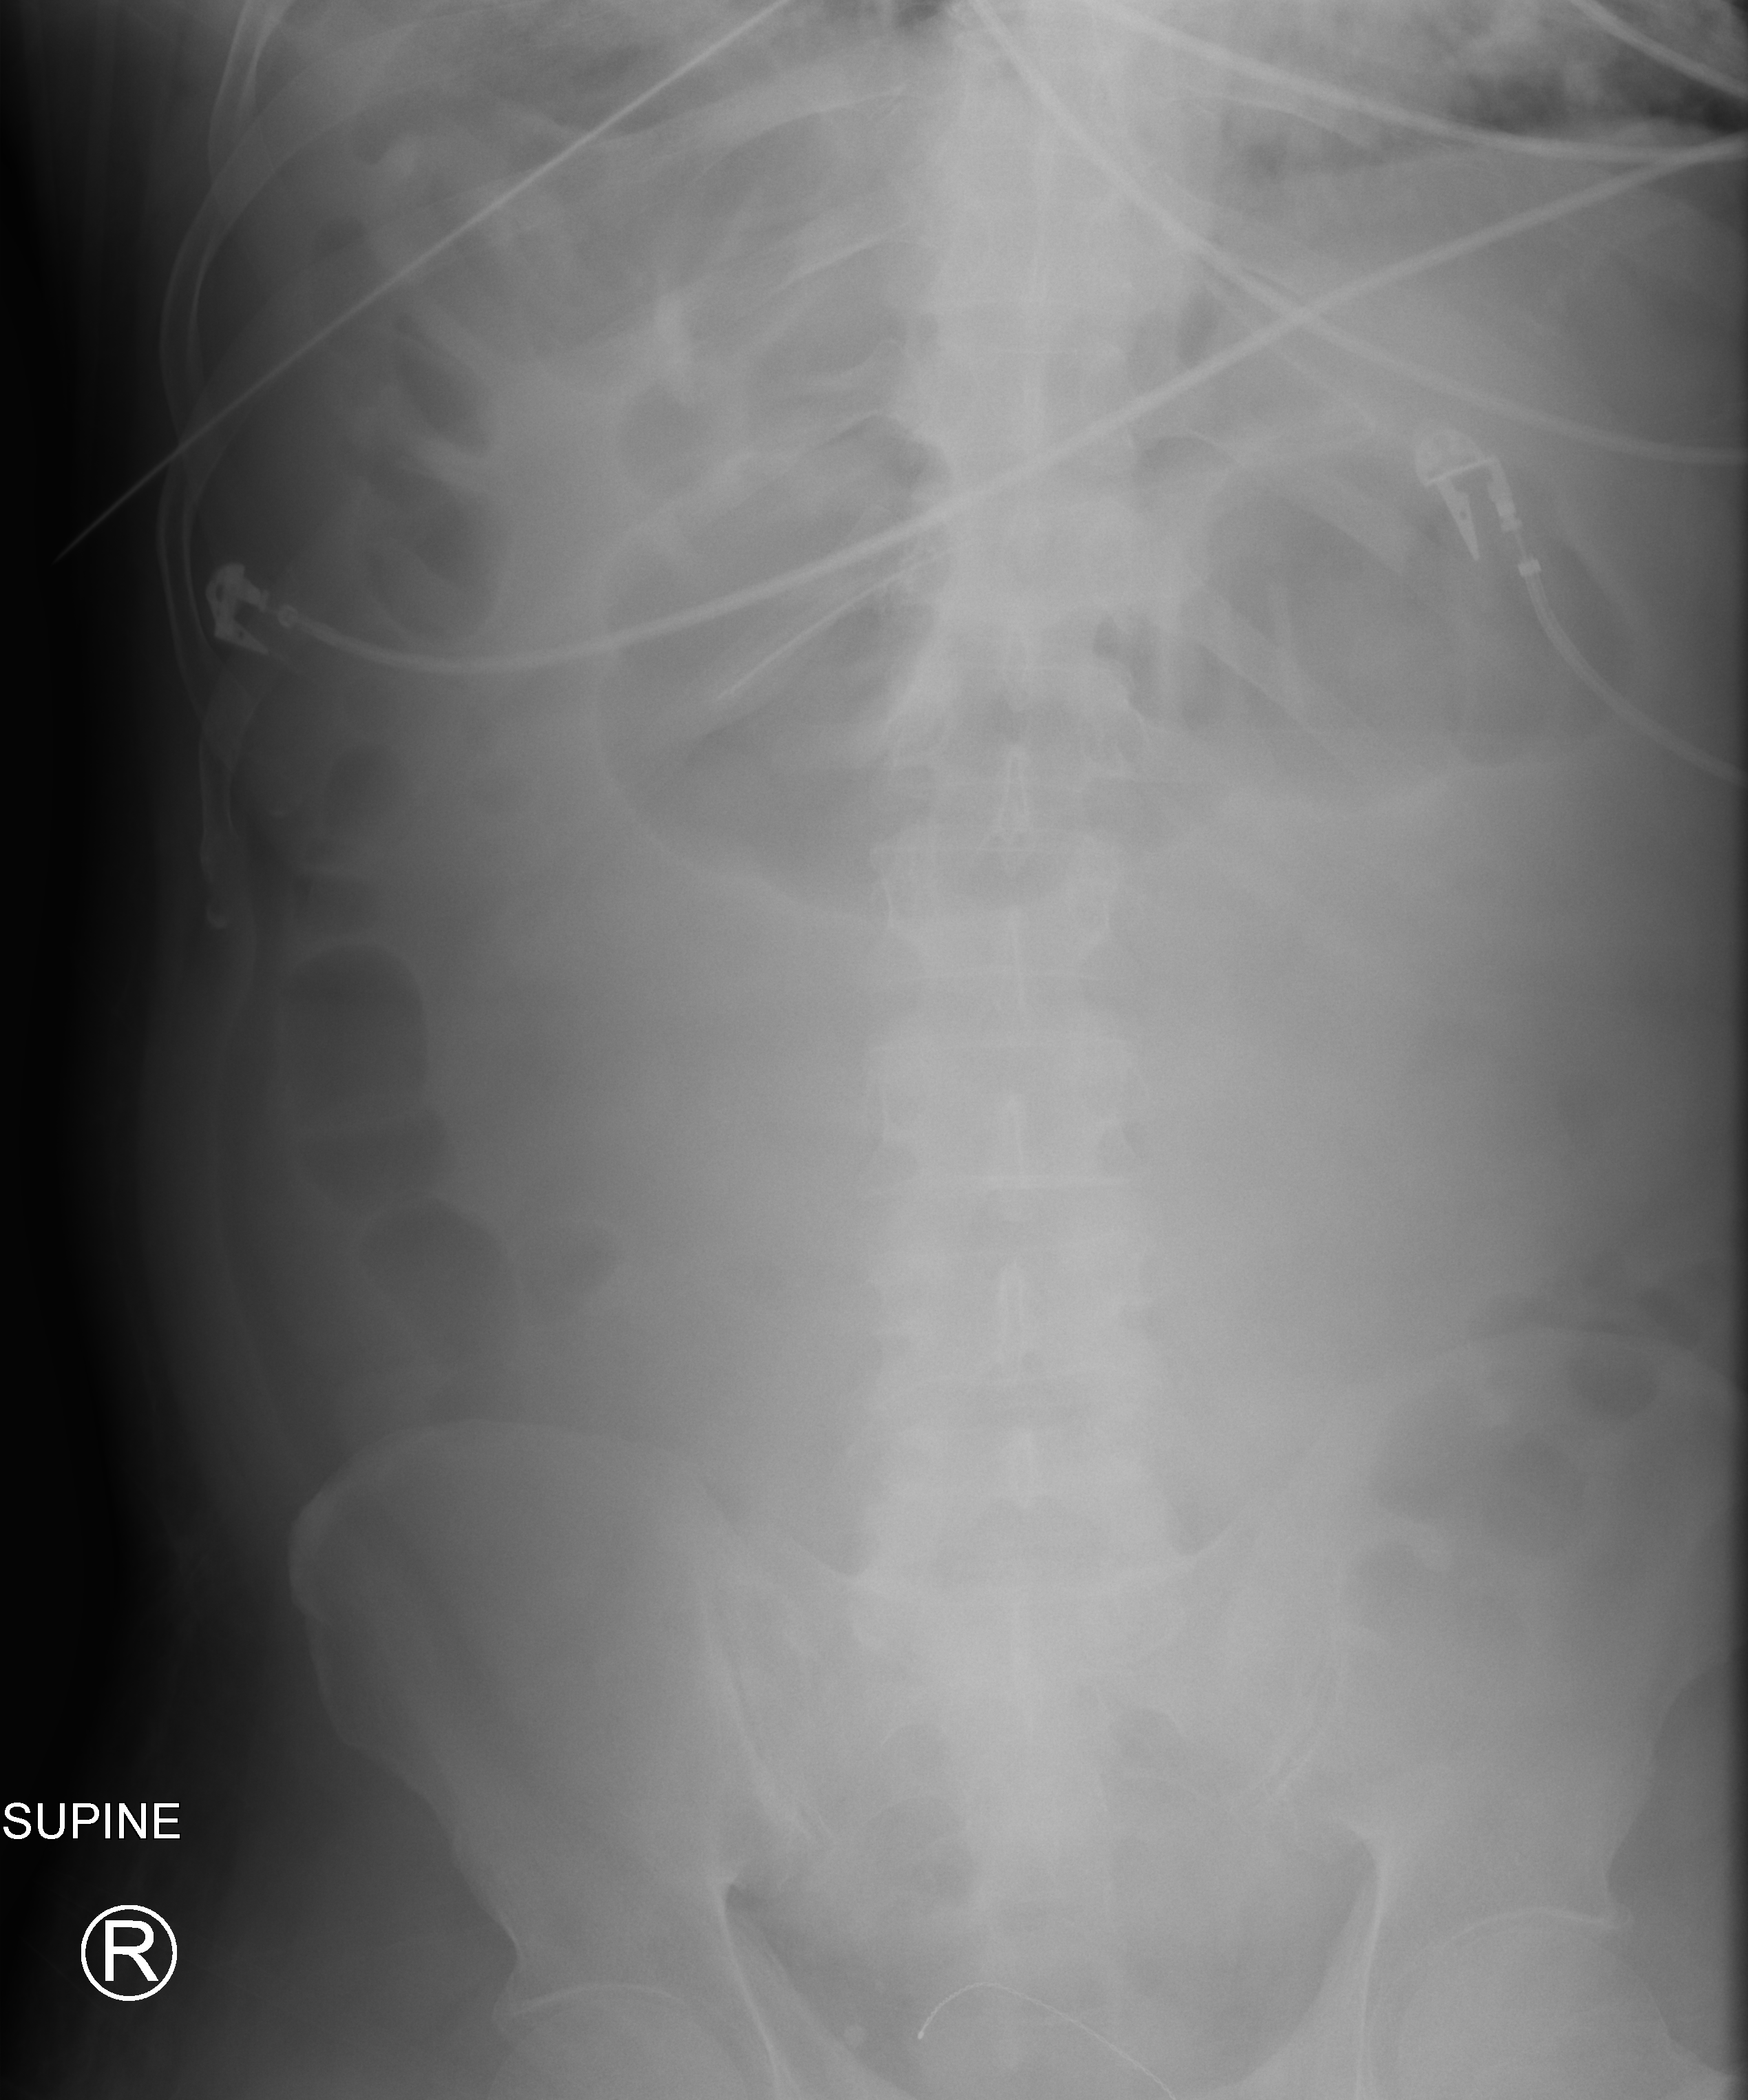
Portable abdomen radiograph; anteroposterior (AP) projection. Patient hospitalised with COVID-19; male, aged 18–59 years.
Admission-level facts for this patient (not findings on this image; timing relative to this image not recorded): COPD (admission record): no; mechanically ventilated during this hospital stay: yes; admitted to intensive care during this hospital stay: yes.